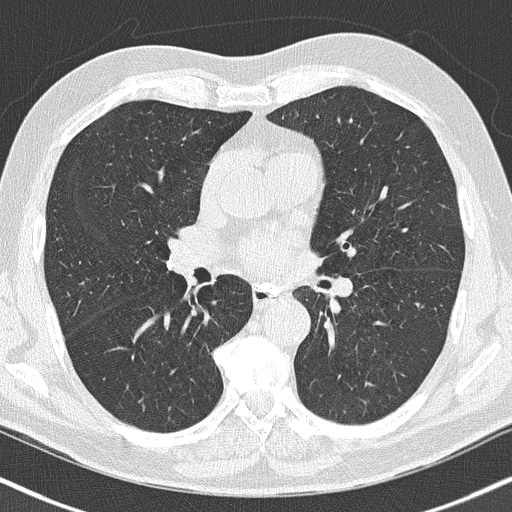
Low-dose screening chest CT, axial slice; baseline screening round; lung window (W 1500 / L -600 HU); 120 kVp; slice 87 of 186 in the series; 512 × 512 image matrix. Male participant, aged 66 years at enrolment.
Expert-annotated lung lesion, box from (x=185, y=270) to (x=209, y=297) px. Reader record for this screening exam (exam-level; its link to the box is not recorded): non-calcified nodule or mass ≥4 mm, right upper lobe, 5 × 4 mm, smooth margins. Lung cancer was diagnosed 778 days after this screen: squamous cell carcinoma, NOS, right lower lobe, poorly differentiated (G3), stage IIA (AJCC 6th edition), 22 mm at pathology.